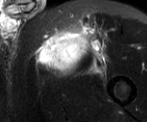
MRI of an extremity soft-tissue mass, one axial slice; position 49 of 52 along the scan axis; T2-weighted fat-saturated; MR volume resampled by the dataset authors to the PET/CT grid (not the native acquisition matrix); 3.27 mm slice thickness; 147 × 122 image matrix. Male patient. Case-level facts recorded for this patient, not image findings: histological type: pleiomorphic liposarcoma; grade: high; site of the primary tumour: left thigh.
Structures marked on this image (expert contour drawn on MRI and transferred to this co-registered scan by the dataset authors):
- gross tumour volume including surrounding oedema: bounding box <39,27,104,74> (left, top, right, bottom; pixels)
- gross tumour volume (mass): <39,32,83,65>